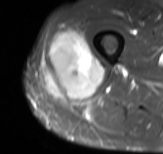
MRI of an extremity soft-tissue mass, one axial slice; slice 34 of 61 in the series (ordered by position); STIR; MR volume resampled by the dataset authors to the PET/CT grid (not the native acquisition matrix); 163 × 154 image matrix, field of view 159 × 150 mm. Male patient. Case-level facts recorded for this patient, not image findings: histological type: poorly differentiated synovial sarcoma; grade: high; site of the primary tumour: right buttock.
Outlined on this slice (expert contour drawn on MRI and transferred to this co-registered scan by the dataset authors):
- gross tumour volume including surrounding oedema: bounding box [x1, y1, x2, y2] px = [41, 30, 104, 99]
- gross tumour volume (mass): [48, 32, 104, 99]